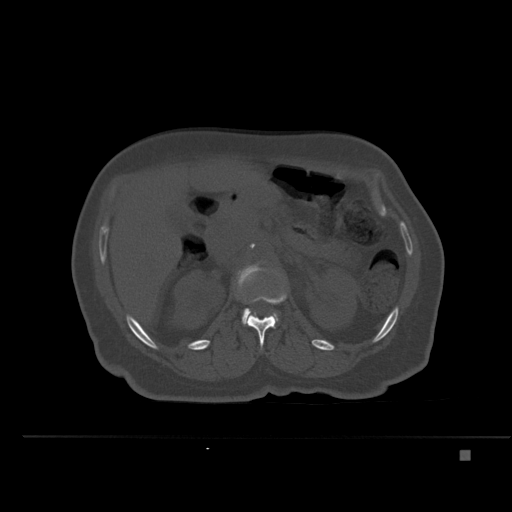
CT including the spine, one axial slice; slice 230 of 477 in the series (ordered by position); bone window (W 1800 / L 400 HU); 1.5 mm slice thickness; 512 × 512 image matrix. Female patient, age 74 years. From the clinical record (not read from this slice): primary cancer: colon.
Outlined on this slice (semi-automatic segmentation, software-assisted and operator-edited):
- L1 vertebra: box from (x=246, y=288) to (x=287, y=347) px
- L2 vertebra: (x=237, y=264)–(x=278, y=324)